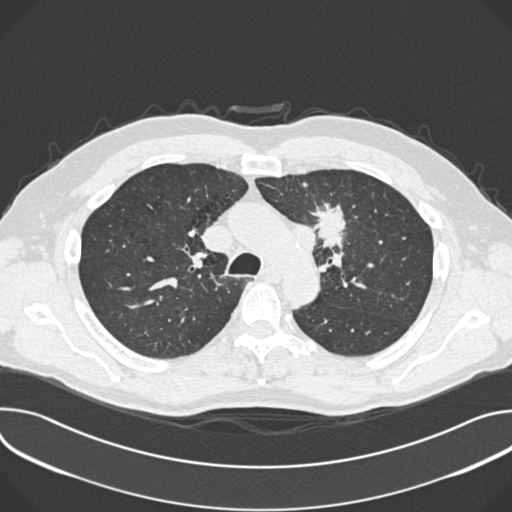
Low-dose screening chest CT, one axial slice. Slice 263 of 361 in the series (ordered by position). 120 kVp. Lung window (W 1500 / L -600 HU). 512 × 512 image matrix.
Outlined on this slice (outlined manually by an expert reader):
- lesion 1 (tumor, upper lobe of left lung): bounding box (x1, y1, x2, y2) in pixels: (313, 207, 346, 247)